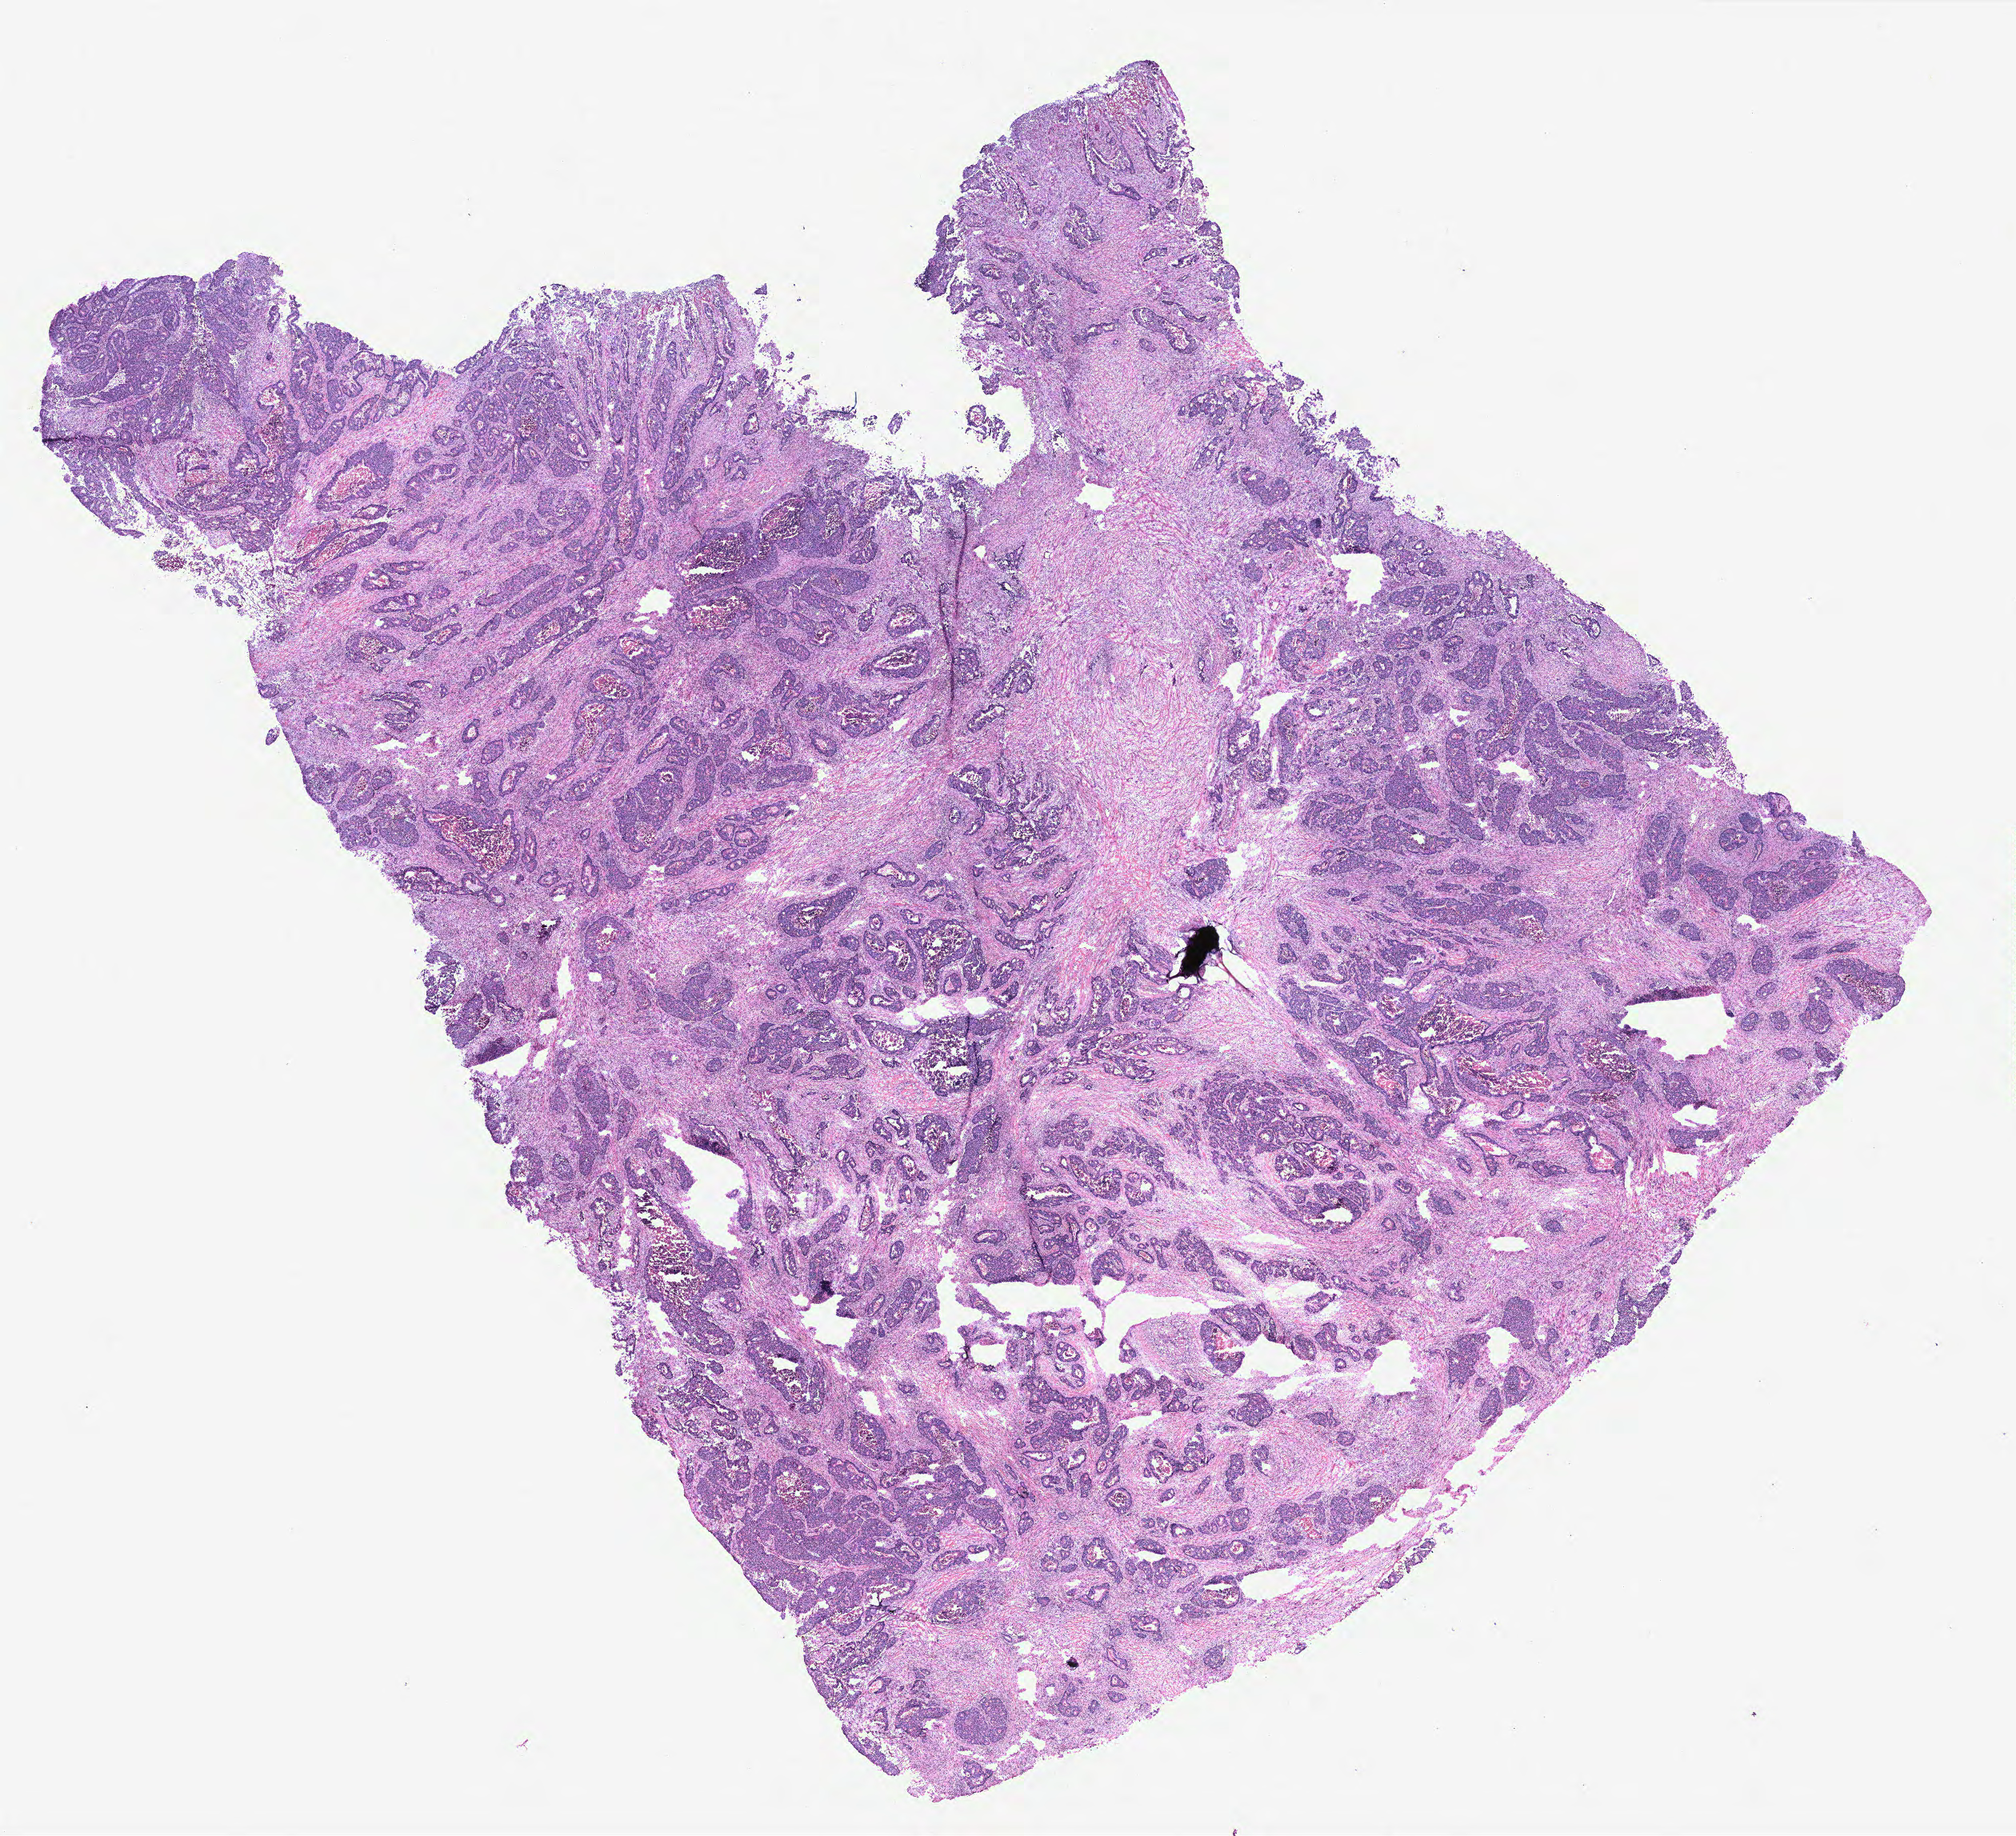
H&E-stained whole-slide image, shown as a low-resolution overview of the whole scanned area (about 20.2 x 18.4 mm). Colon, normal (non-tumour) tissue. 64-year-old female patient.
This section: normal (non-tumour) tissue from the same patient. Patient diagnosis: Adenocarcinoma, NOS.